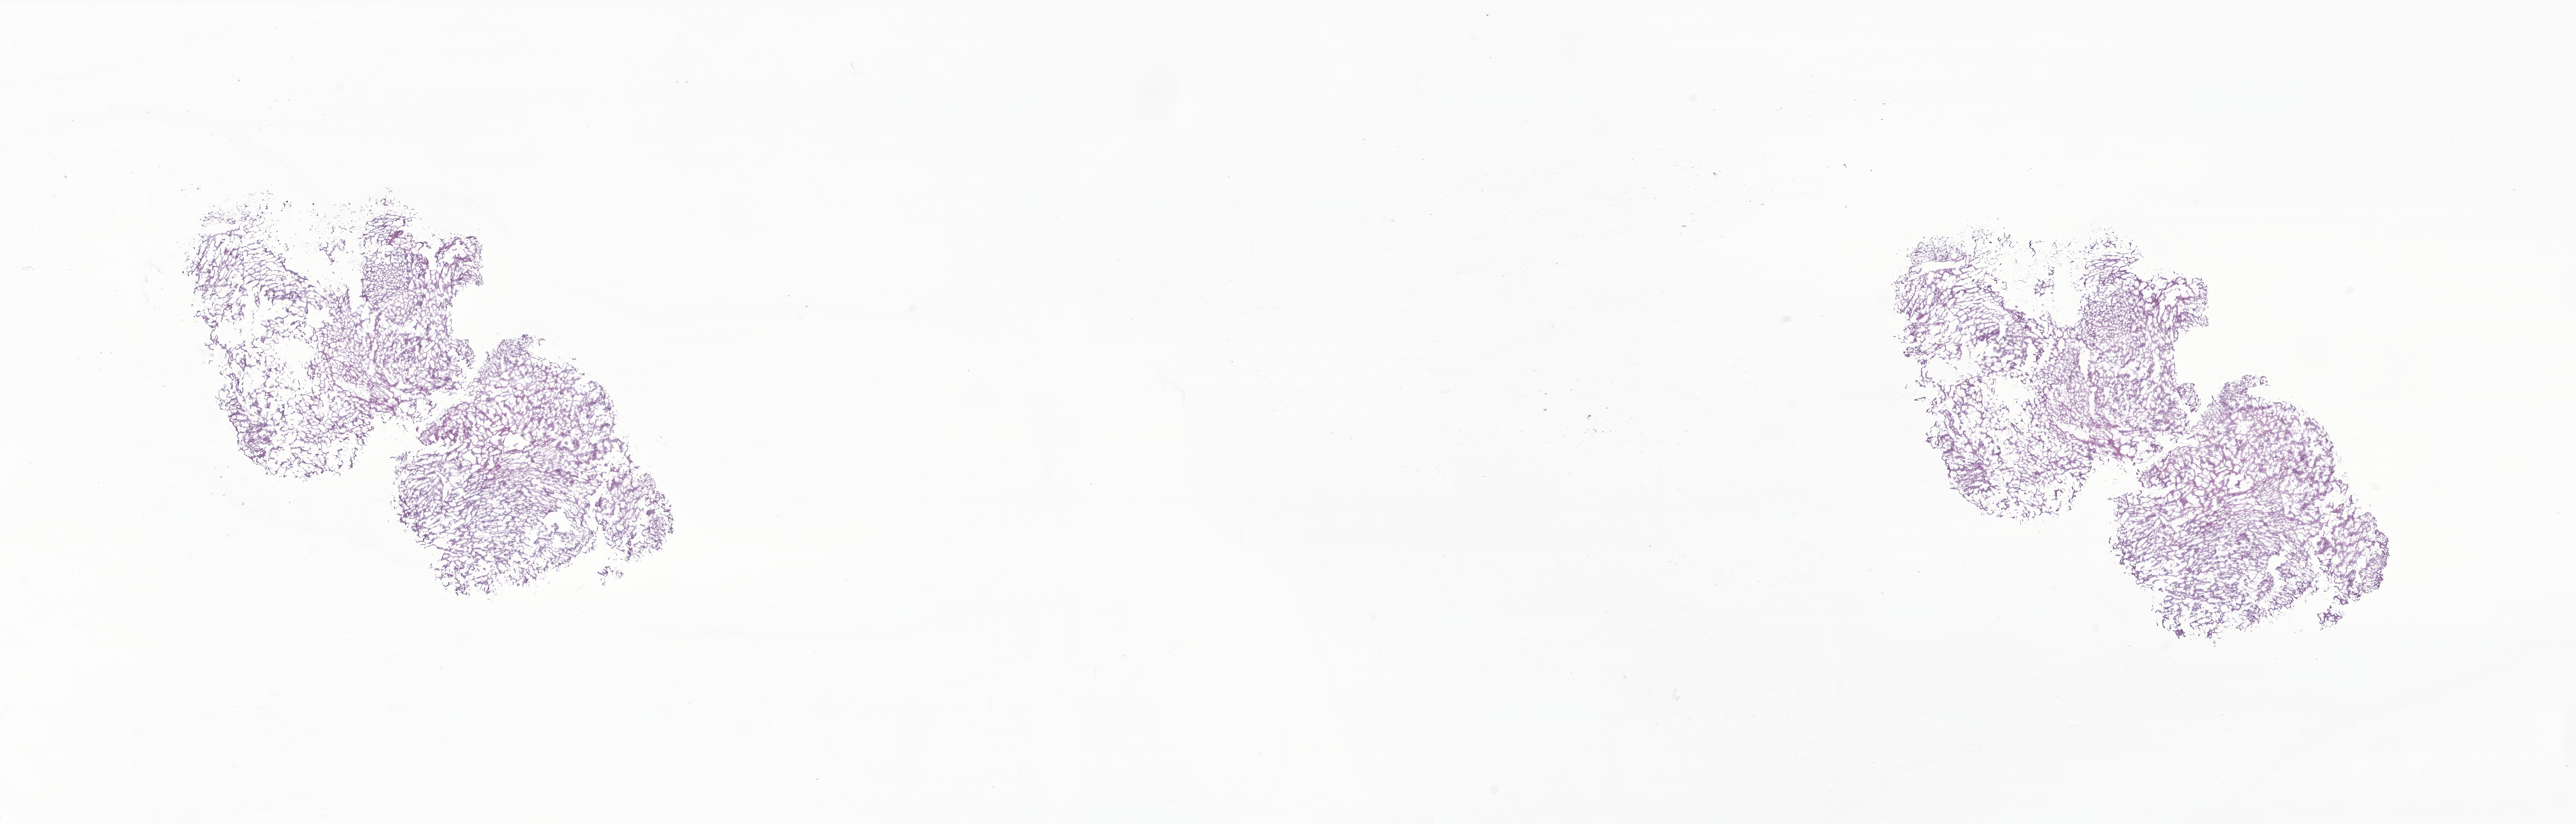
Whole-slide image, haematoxylin and eosin stain of tumor tissue from the cerebellum, shown as a low-resolution overview of the whole scanned area (about 26.9 x 8.6 mm), frozen section (OCT-embedded). Female patient, age 326 days.
• diagnosis (ICD-O-3 morphology term): Ependymoma, NOS